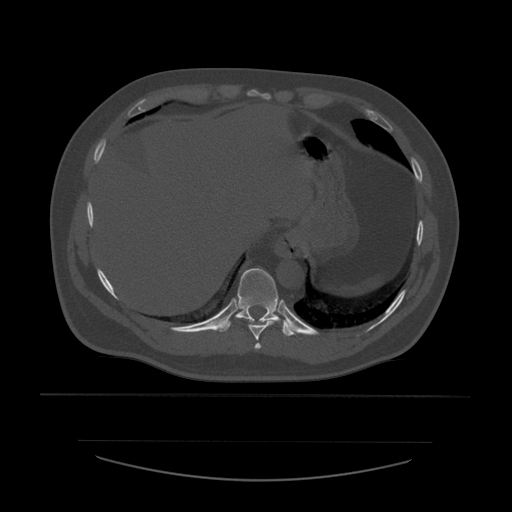
CT including the spine, one axial slice. Position 306 of 532 along the scan axis. Reconstruction kernel STANDARD. Bone window (W 1800 / L 400 HU). 512 × 512 image matrix, field of view 441 × 441 mm. Patient age 44 years. From the clinical record (not read from this slice): primary cancer: soft tissue sarcoma.
Outlined on this slice (semi-automatic segmentation, software-assisted and operator-edited):
- T10 vertebra: bounding box [x1, y1, x2, y2] px = [216, 268, 298, 337]
- T8 vertebra: [254, 343, 262, 350]
- T9 vertebra: [248, 320, 277, 341]